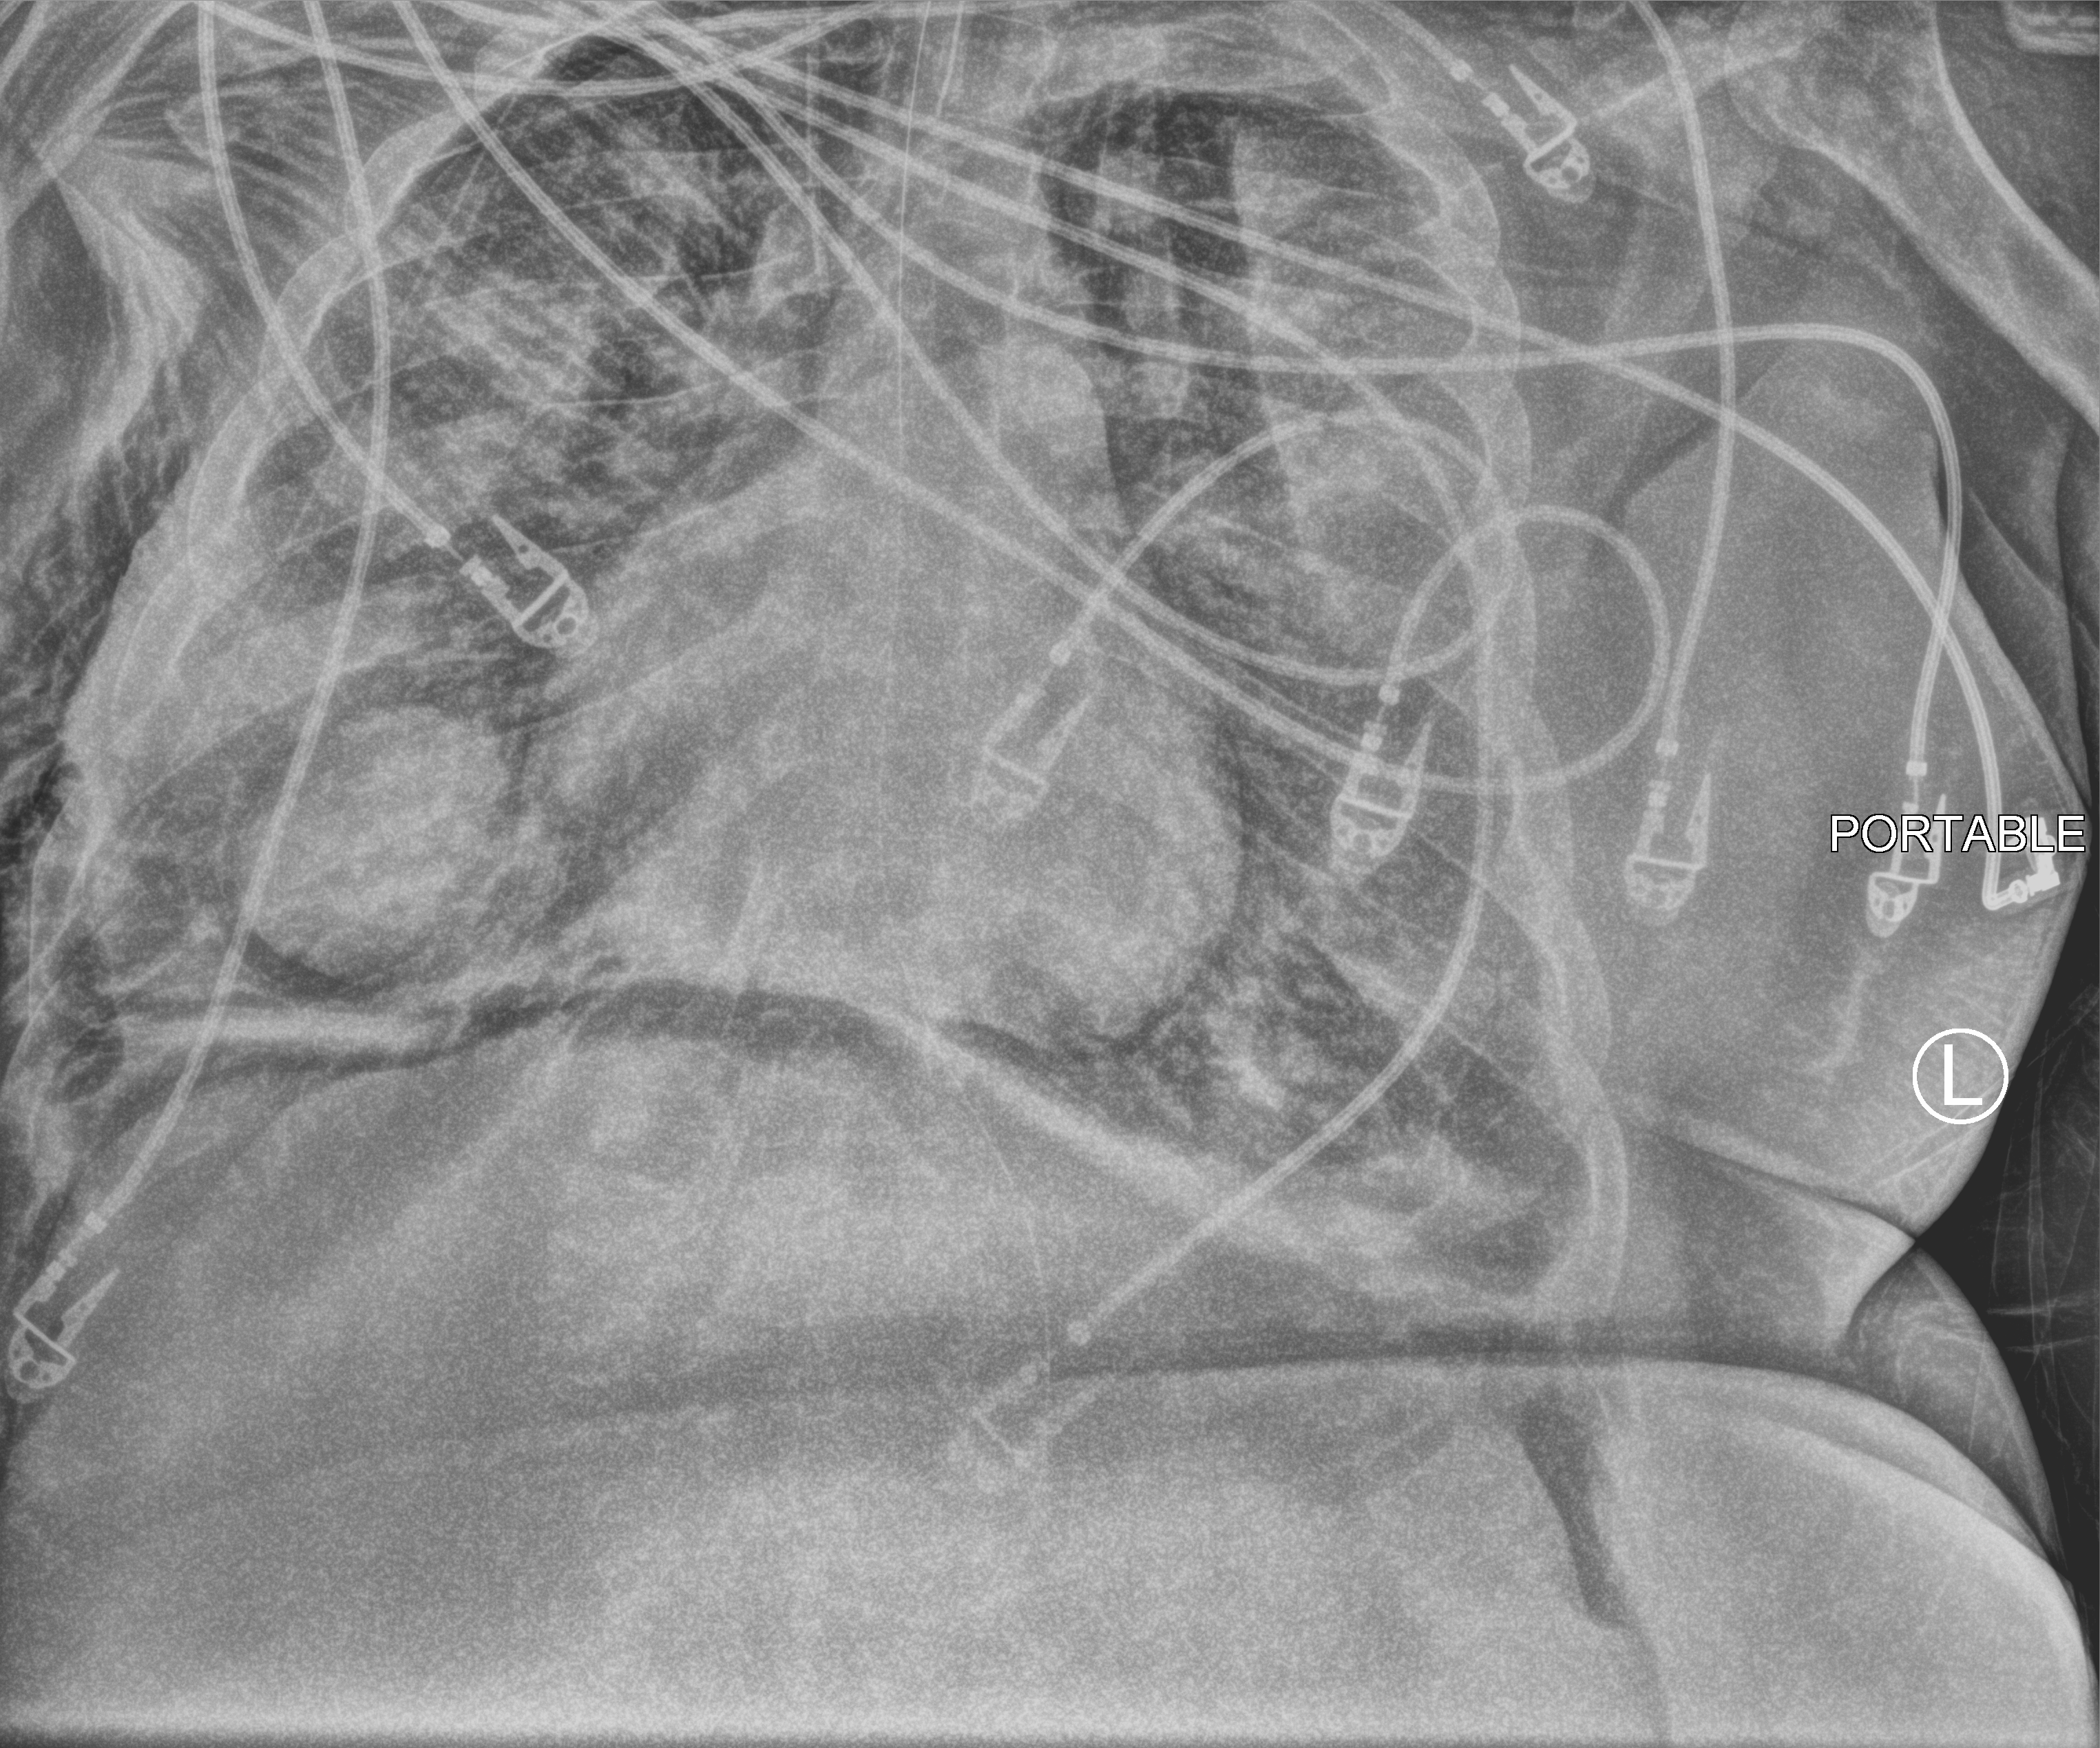
Chest X-ray (portable); anteroposterior (AP) projection. Adult patient hospitalised with COVID-19, age 18–59 years.
Admission-level facts for this patient (not findings on this image; timing relative to this image not recorded):
- diabetes (admission record): no
- length of hospital stay: 15 days